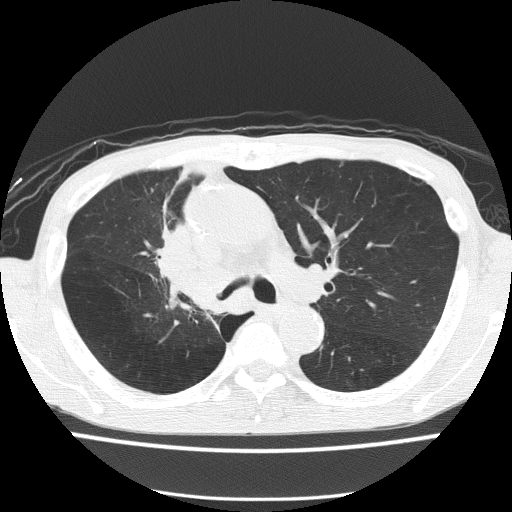
Chest CT (low-dose screening protocol), one axial image, baseline annual screen, lung window (W 1500 / L -600 HU), lung (sharp) reconstruction kernel (FC51), slice 53 of 150 in the series. Male participant, aged 59 years at enrolment. Former smoker at enrolment.
Lesion marked by an expert reader, bounding box <140,231,233,322> (left, top, right, bottom; pixels). The screening reader recorded 5 non-calcified nodules or masses ≥4 mm on this exam (left upper lobe, left upper lobe, left upper lobe, right middle lobe, right lower lobe); which of them this box marks is not recorded. Official screen result: positive, change unspecified: nodule(s) >= 4 mm or enlarging nodule(s), mass(es), or other non-specific abnormalities suspicious for lung cancer. Lung cancer was diagnosed 72 days after this screen: squamous cell carcinoma, NOS, right upper lobe, moderately differentiated (G2), stage IV (AJCC 6th edition).